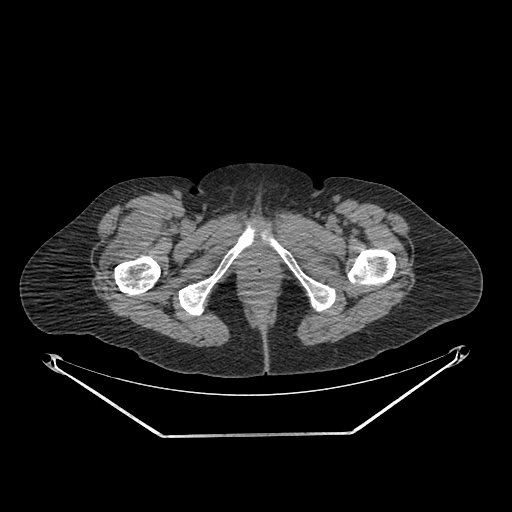
CT of an extremity soft-tissue mass (from a PET/CT study), one axial slice. Slice 282 of 311 in the series (ordered by position). 140 kVp. Soft-tissue window (W 400 / L 40 HU). 512 × 512 image matrix, field of view 500 × 500 mm. Female patient. From the clinical record (not read from this slice): histological type: pleiomorphic undifferentiated sarcoma; grade: high; site of the primary tumour: right quadricep.
Outlined on this slice (expert contour drawn on MRI and transferred to this co-registered scan by the dataset authors):
- tumour plus oedema (research contour): bounding box <101,205,168,275> (left, top, right, bottom; pixels)
- tumour (research contour): <116,205,168,250>